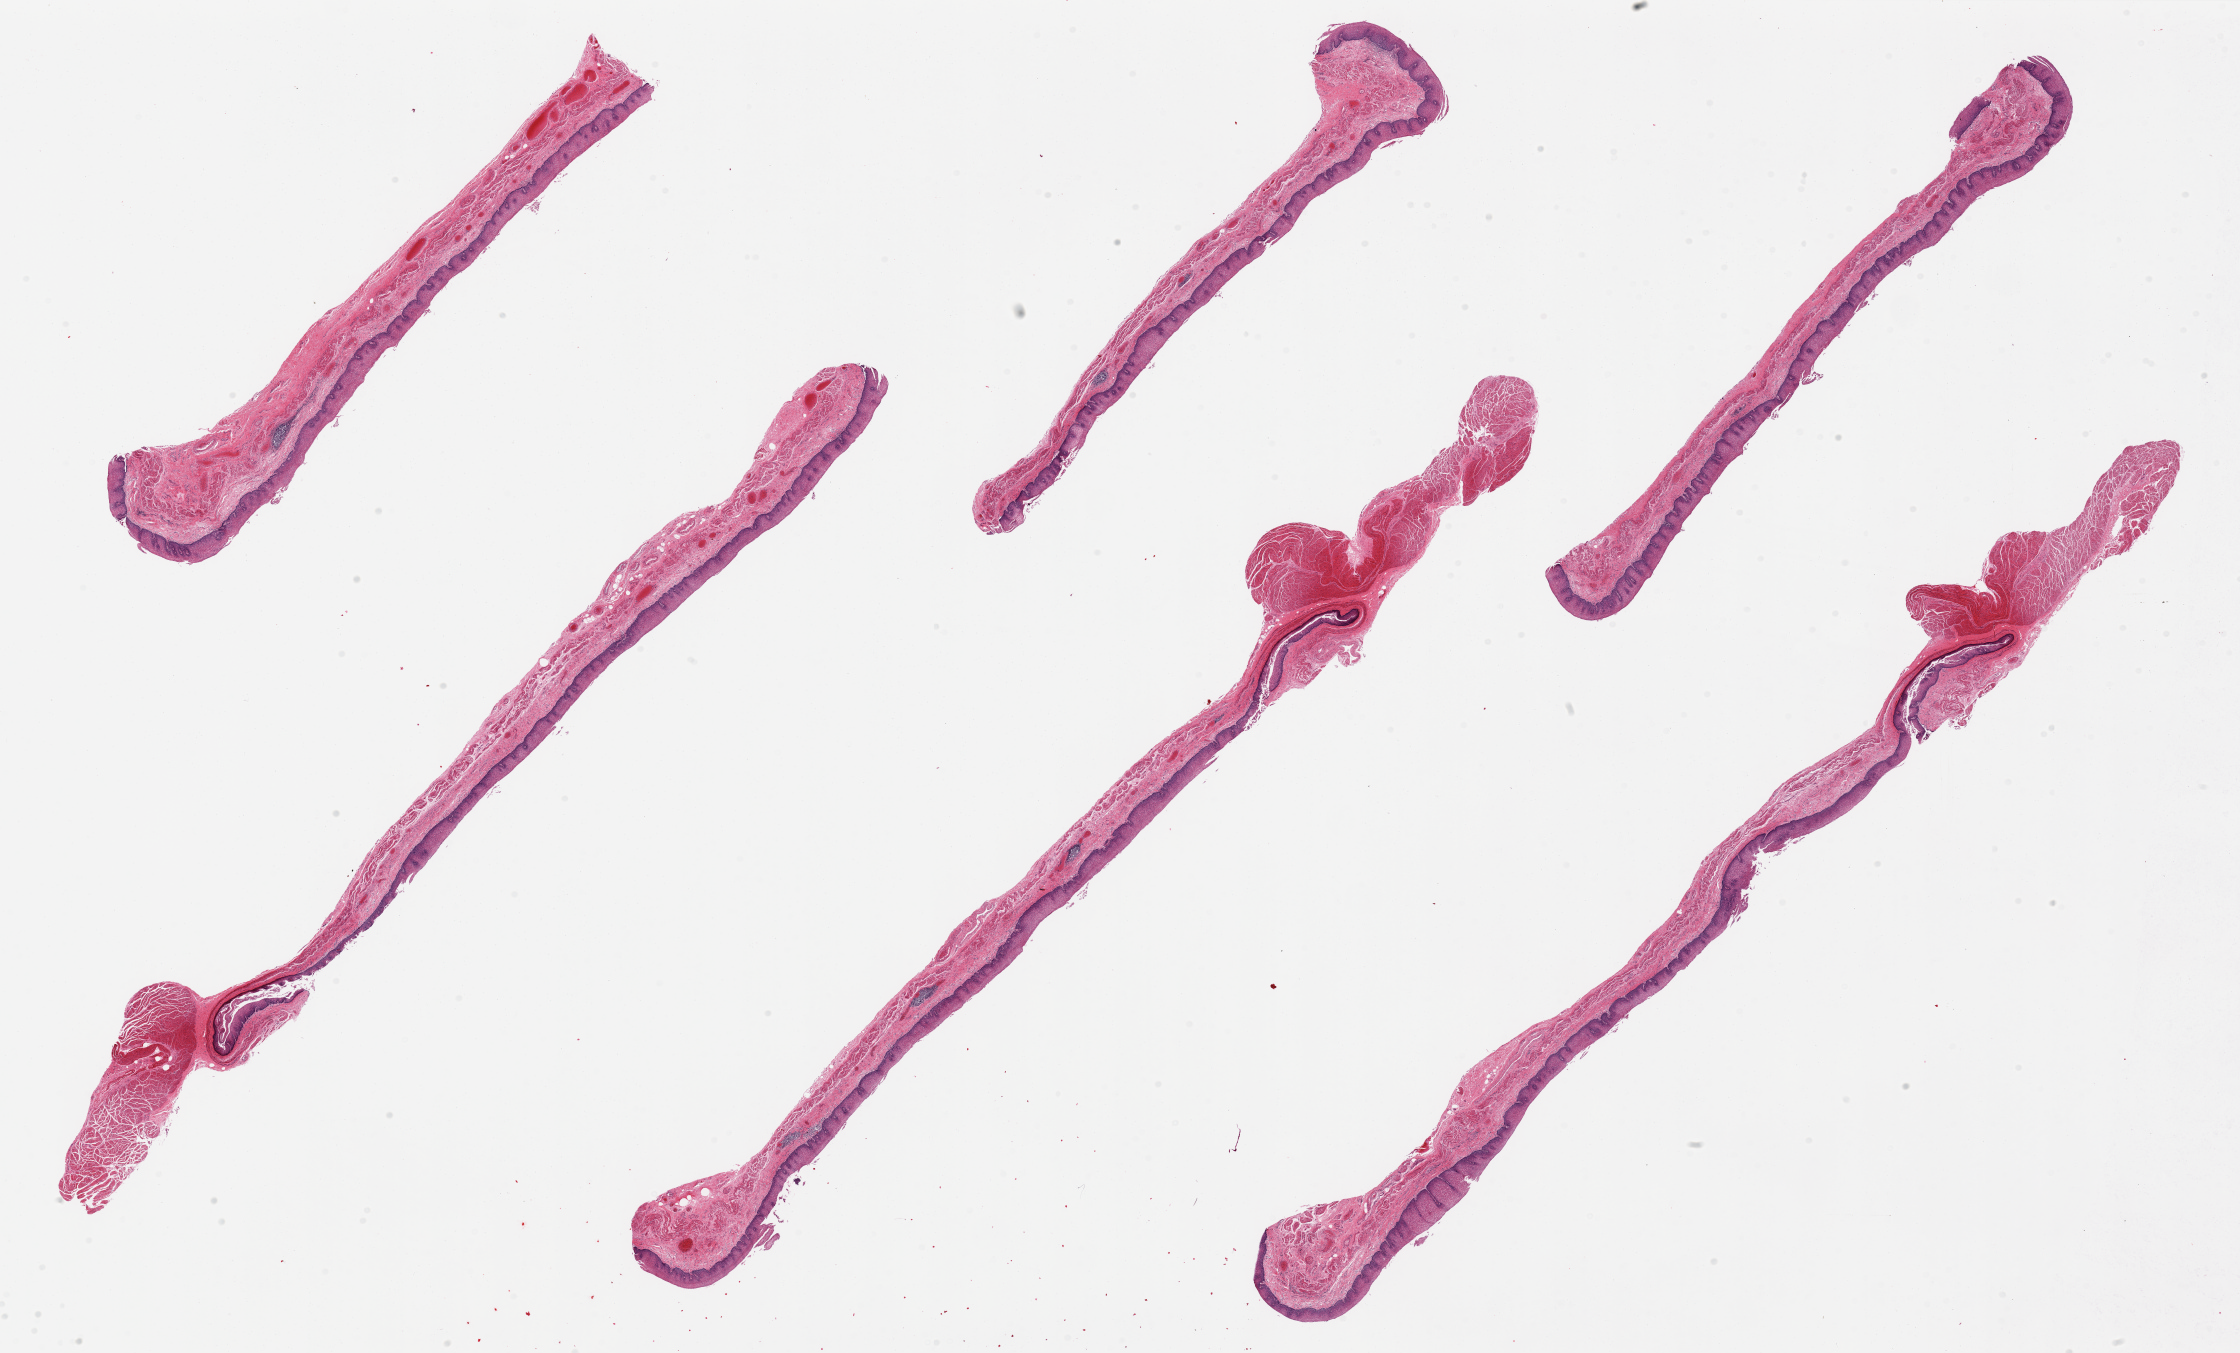
Digitized haematoxylin and eosin-stained section — low-resolution overview of the scanned area, about 35.4 x 21.4 mm (acquisition: 20x scan). PAXgene-fixed paraffin-embedded (PFPE) section. Section of esophageal mucous membrane (target tissue). Tissue donor sample.
* review note (as recorded): 6 pieces; well dissected mucosa